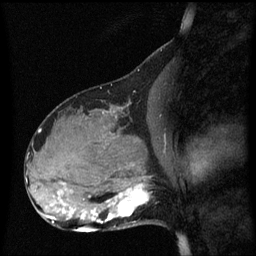
Breast MRI (dynamic contrast-enhanced), one sagittal slice; position 27 of 60 along the scan axis; dynamic contrast-enhanced series, image 2 of 3 at this slice position (ordered by acquisition); 1.5 T; TE 4.2 ms, TR 8.4 ms; 256 × 256 image matrix, field of view 210 × 210 mm. Female patient, age 31 years. From the clinical record (not read from this slice): setting: breast cancer imaged before/during neoadjuvant chemotherapy; receptor status: HR-positive, HER2-negative.
Annotated regions visible in this slice (semi-automatic segmentation, software-assisted and operator-edited):
- analysis volume of interest (the breast-tissue region the enhancement analysis was run in; not a lesion): bounding box [x1, y1, x2, y2] px = [98, 175, 155, 228]
- tumour enhancement mask (voxels above the 70 % enhancement threshold inside the analysis volume of interest): [98, 184, 150, 224]